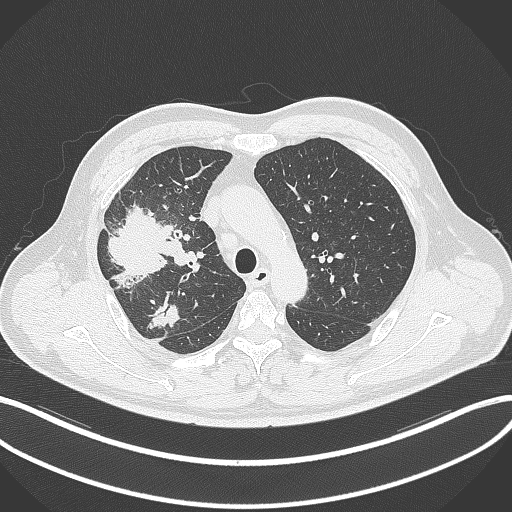
Chest CT, one axial slice; position 240 of 348 along the scan axis; reconstruction kernel B70f; 120 kVp; lung window (W 1500 / L -600 HU); 1 mm slice thickness; 512 × 512 image matrix, field of view 400 × 400 mm. Male patient, age 55 years. From the clinical record (not read from this slice): clinical TNM (as recorded): T3 N2 M1.
Outlined on this slice (rectangle marked by the reading radiologist):
- lung tumour (recorded histology: adenocarcinoma): box from (x=97, y=201) to (x=174, y=286) px